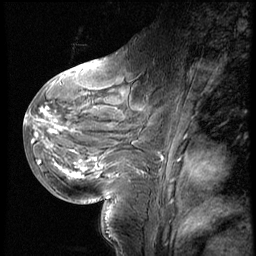
Breast MRI (dynamic contrast-enhanced), one sagittal slice; position 26 of 60 along the scan axis; 3 images stored at this slice position (order not interpretable as contrast timing); 1.5 T; TE 4.2 ms, TR 8.9 ms; 2.5 mm slice thickness; 256 × 256 image matrix, field of view 200 × 200 mm. Female patient, age 29 years. Case-level facts recorded for this patient, not image findings: setting: breast cancer imaged before/during neoadjuvant chemotherapy.
Annotated regions visible in this slice (semi-automatically segmented with operator editing):
- analysis volume of interest (the breast-tissue region the enhancement analysis was run in; not a lesion): bounding box (x1, y1, x2, y2) in pixels: (29, 57, 166, 200)
- tumour enhancement mask (voxels above the 140 % enhancement threshold inside the analysis volume of interest): (33, 69, 101, 179)